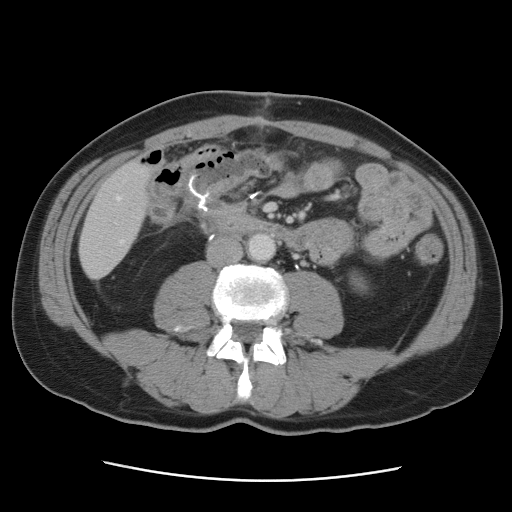
Contrast-enhanced abdominal CT, one axial slice. Intravenous contrast given. Soft-tissue window (W 400 / L 40 HU). 5 mm slice thickness. 512 × 512 image matrix, field of view 366 × 366 mm. Male patient, age 59 years. From the clinical record (not read from this slice): diagnosis: colorectal cancer liver metastases, imaged before liver resection; multiple liver metastases: yes; largest metastasis: 0.6 cm; disease in both lobes: yes.
Annotated regions visible in this slice (manually delineated by an expert):
- hepatic veins: bounding box [x1, y1, x2, y2] px = [117, 197, 124, 244]
- liver: [80, 161, 154, 278]
- planned liver remnant (the part of the liver to remain after resection): [80, 161, 154, 257]